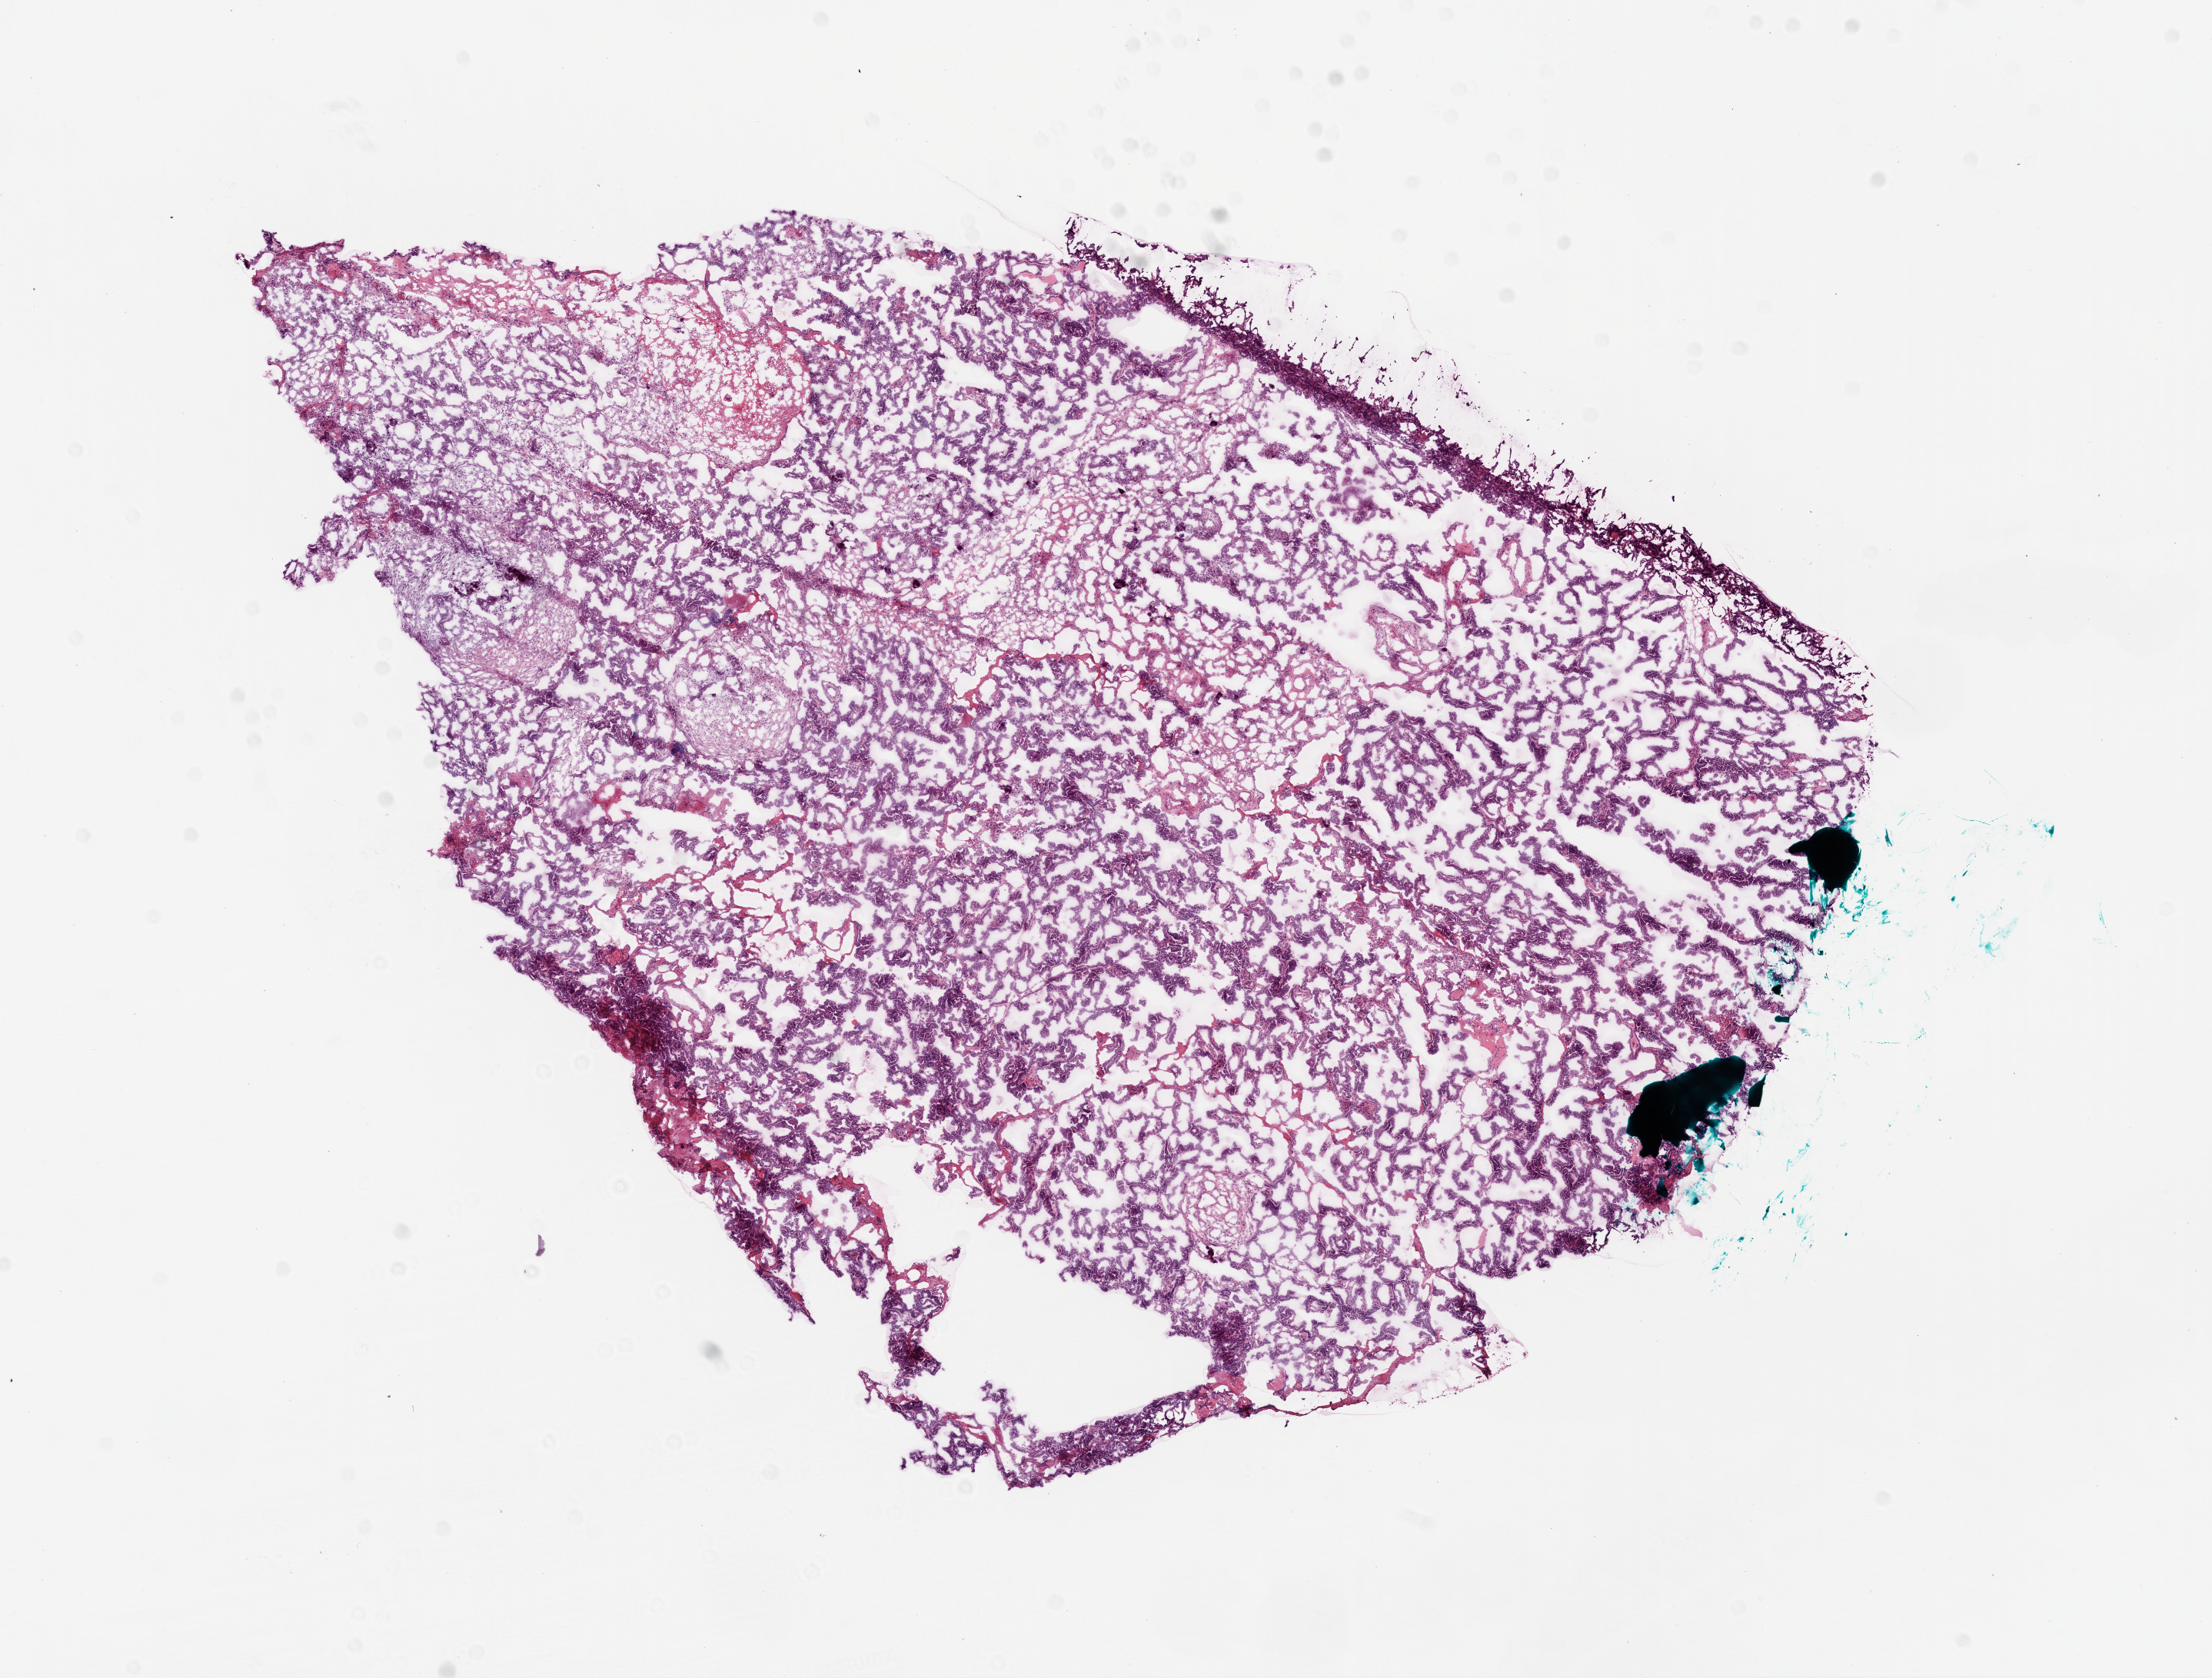
Whole-slide histology image, H&E-stained — whole scanned area (about 11.6 x 8.8 mm) shown as a low-resolution overview. Frozen section from the bottom of the tissue portion. Primary tumour sample from the ovary. Patient: female, age at initial diagnosis 63 years. Slide review estimates, as recorded: tumour cells 98%, tumour nuclei 99%.
Pathologic diagnosis: Serous cystadenocarcinoma, NOS.